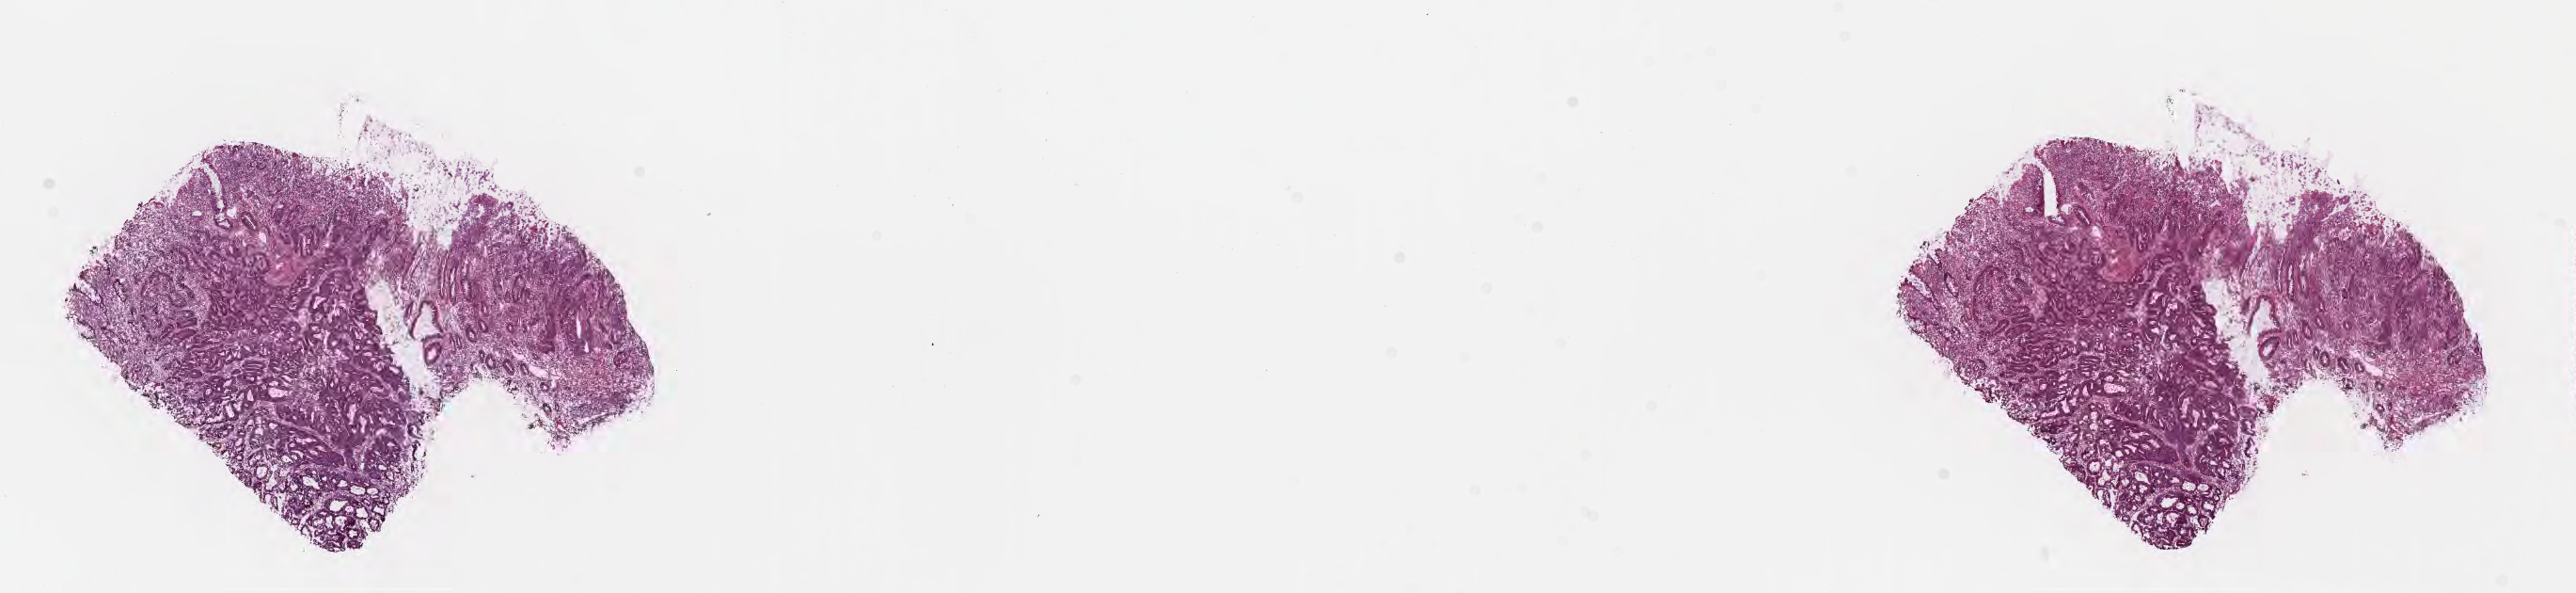
Digitized hematoxylin and eosin (H&E)-stained section — low-resolution overview of the scanned area, about 22.1 x 5.1 mm. Cryosection. Specimen: primary tumor. Site: rectum. Patient: male, age at initial diagnosis 54 years. Tumor grade: G2 (moderately differentiated). Composition of this section per pathologist review: tumor cells 75%, tumor nuclei 75%, stromal cells 18%, necrosis 2%, normal cells 5%. Infiltration values recorded for this section: lymphocyte infiltration 4%, monocyte infiltration 2%, neutrophil infiltration 6%.
• AJCC pathologic stage: Stage IIA
• section: bottom of the tissue portion
• diagnosis: Adenocarcinoma, NOS